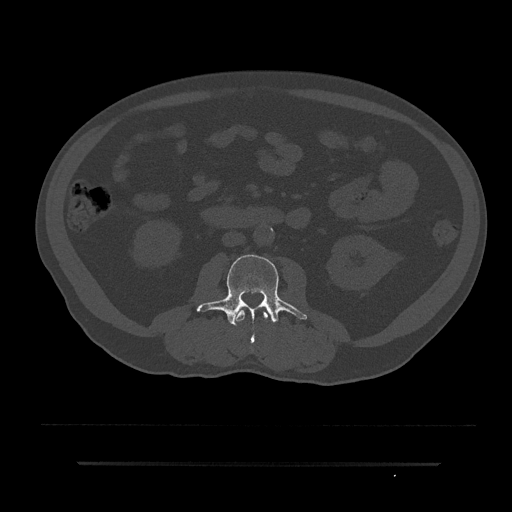
CT including the spine, one axial slice; slice 17 of 797 in the series (ordered by position); bone window (W 1800 / L 400 HU); 0.5 mm slice thickness; 512 × 512 image matrix, field of view 464 × 464 mm. Patient: male, 59 years. Case-level facts recorded for this patient, not image findings: primary cancer: bile ducts; vertebrae with lytic lesions (as recorded): T10.
Outlined on this slice (semi-automatically segmented with operator editing):
- L2 vertebra: box from (x=234, y=308) to (x=268, y=322) px
- L3 vertebra: (x=197, y=255)–(x=307, y=342)